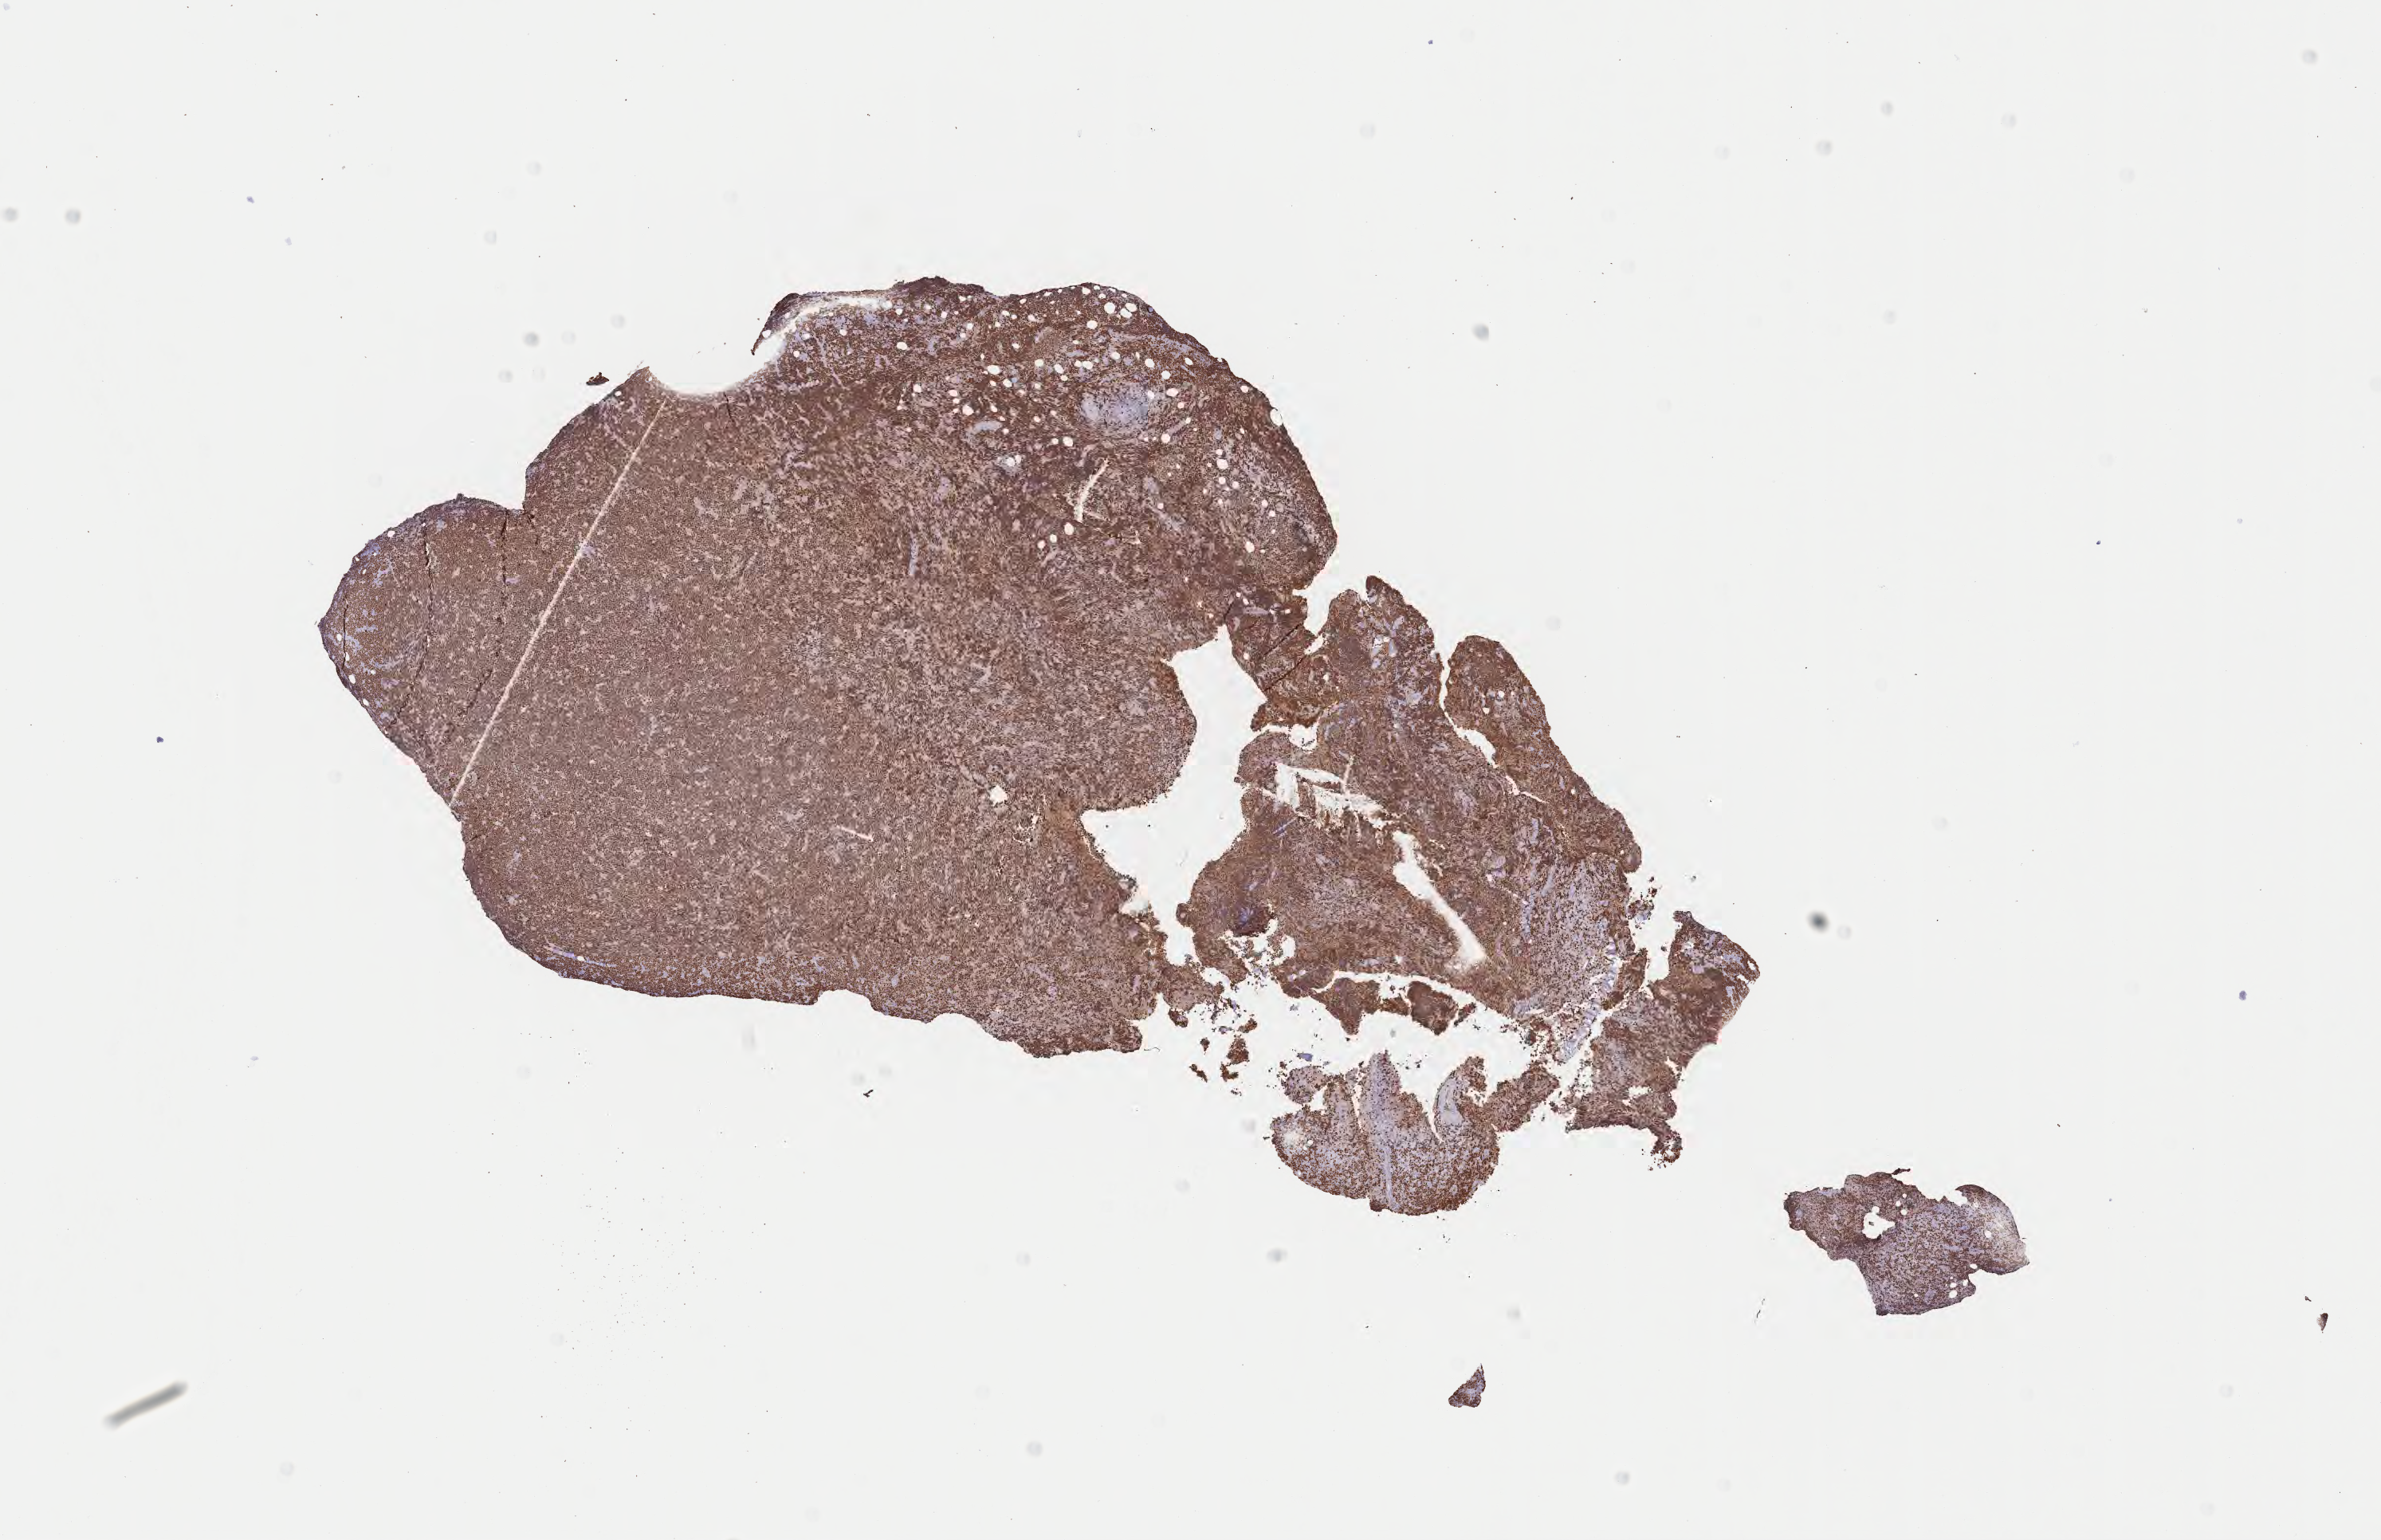
Immunohistochemistry (IHC) whole-slide image stained for Ki-67, whole scanned area (about 12.1 x 7.8 mm) shown as a low-resolution overview. Specimen: tumor tissue. Patient female; age 40 years.
• histologic diagnosis: Burkitt lymphoma, NOS